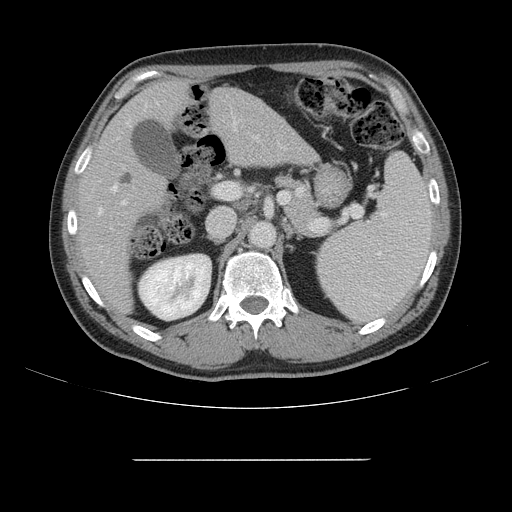
Contrast-enhanced abdominal CT, one axial slice; position 88 of 164 along the scan axis; intravenous contrast given; soft-tissue window (W 400 / L 40 HU); 2.5 mm slice thickness; 512 × 512 image matrix. Male patient, age 54 years. Case-level facts recorded for this patient, not image findings: diagnosis: colorectal cancer liver metastases, imaged before liver resection; multiple liver metastases: yes; largest metastasis: 1 cm.
Outlined on this slice (expert manual segmentation):
- hepatic veins: bounding box (x1, y1, x2, y2) in pixels: (99, 184, 118, 212)
- liver: (81, 81, 313, 310)
- planned liver remnant (the part of the liver to remain after resection): (81, 81, 230, 309)
- portal vein (with intrahepatic branches): (122, 122, 259, 205)